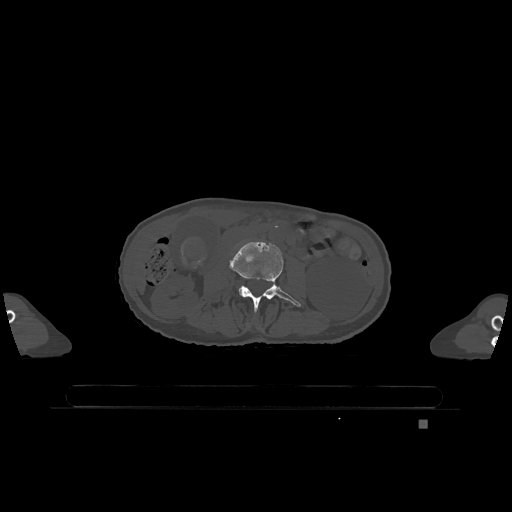
CT including the spine, one axial slice. Position 354 of 1317 along the scan axis. Bone window (W 1800 / L 400 HU). 0.5 mm slice thickness. 512 × 512 image matrix, field of view 500 × 500 mm. Patient: female, 74 years. From the clinical record (not read from this slice): primary cancer: lung; vertebrae with lytic lesions (as recorded): T1, T4, T5, T6, L4, L5.
Outlined on this slice (semi-automatically segmented with operator editing):
- L3 vertebra: bounding box <230,241,301,312> (left, top, right, bottom; pixels)